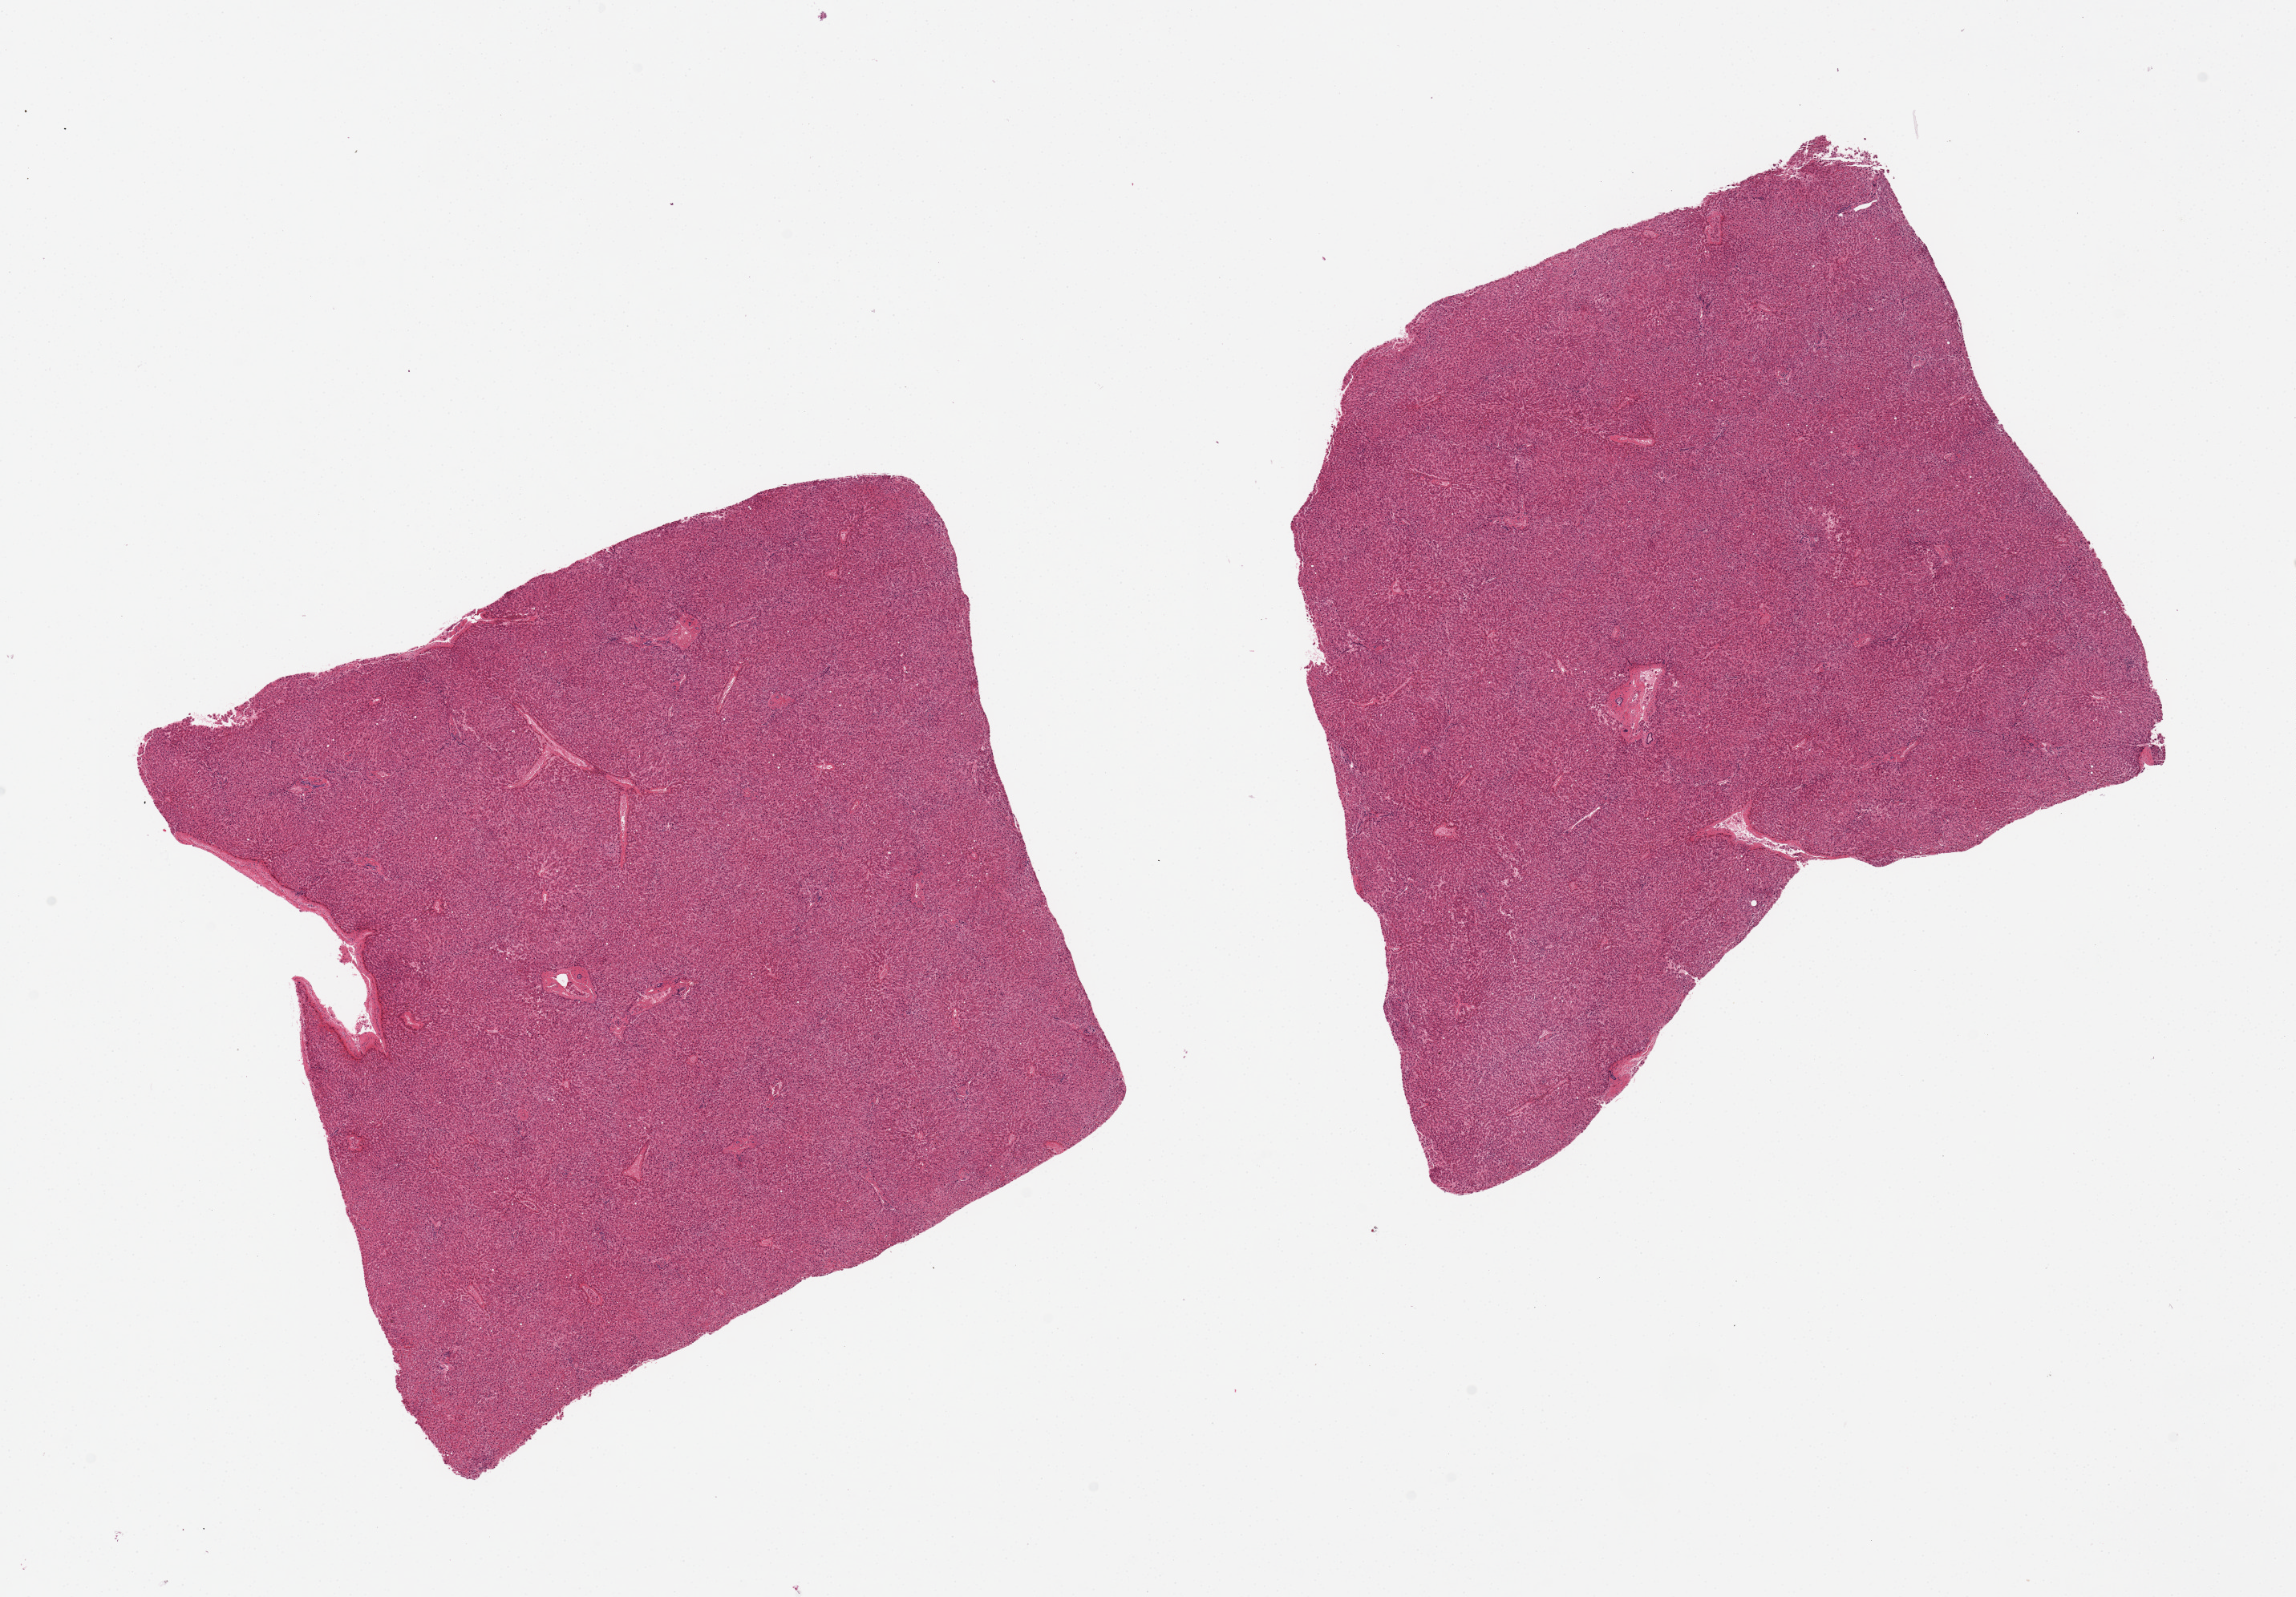
H&E whole-slide image, brightfield — a low-resolution overview of the entire scanned area, about 22.6 x 15.8 mm. PAXgene-fixed, paraffin-embedded tissue. Section of liver (target tissue). Donor tissue sample. Donor sex: female.
Pathologist's review note for this sample: 2 pieces, minimal steatosis, reasonably well-preserved.